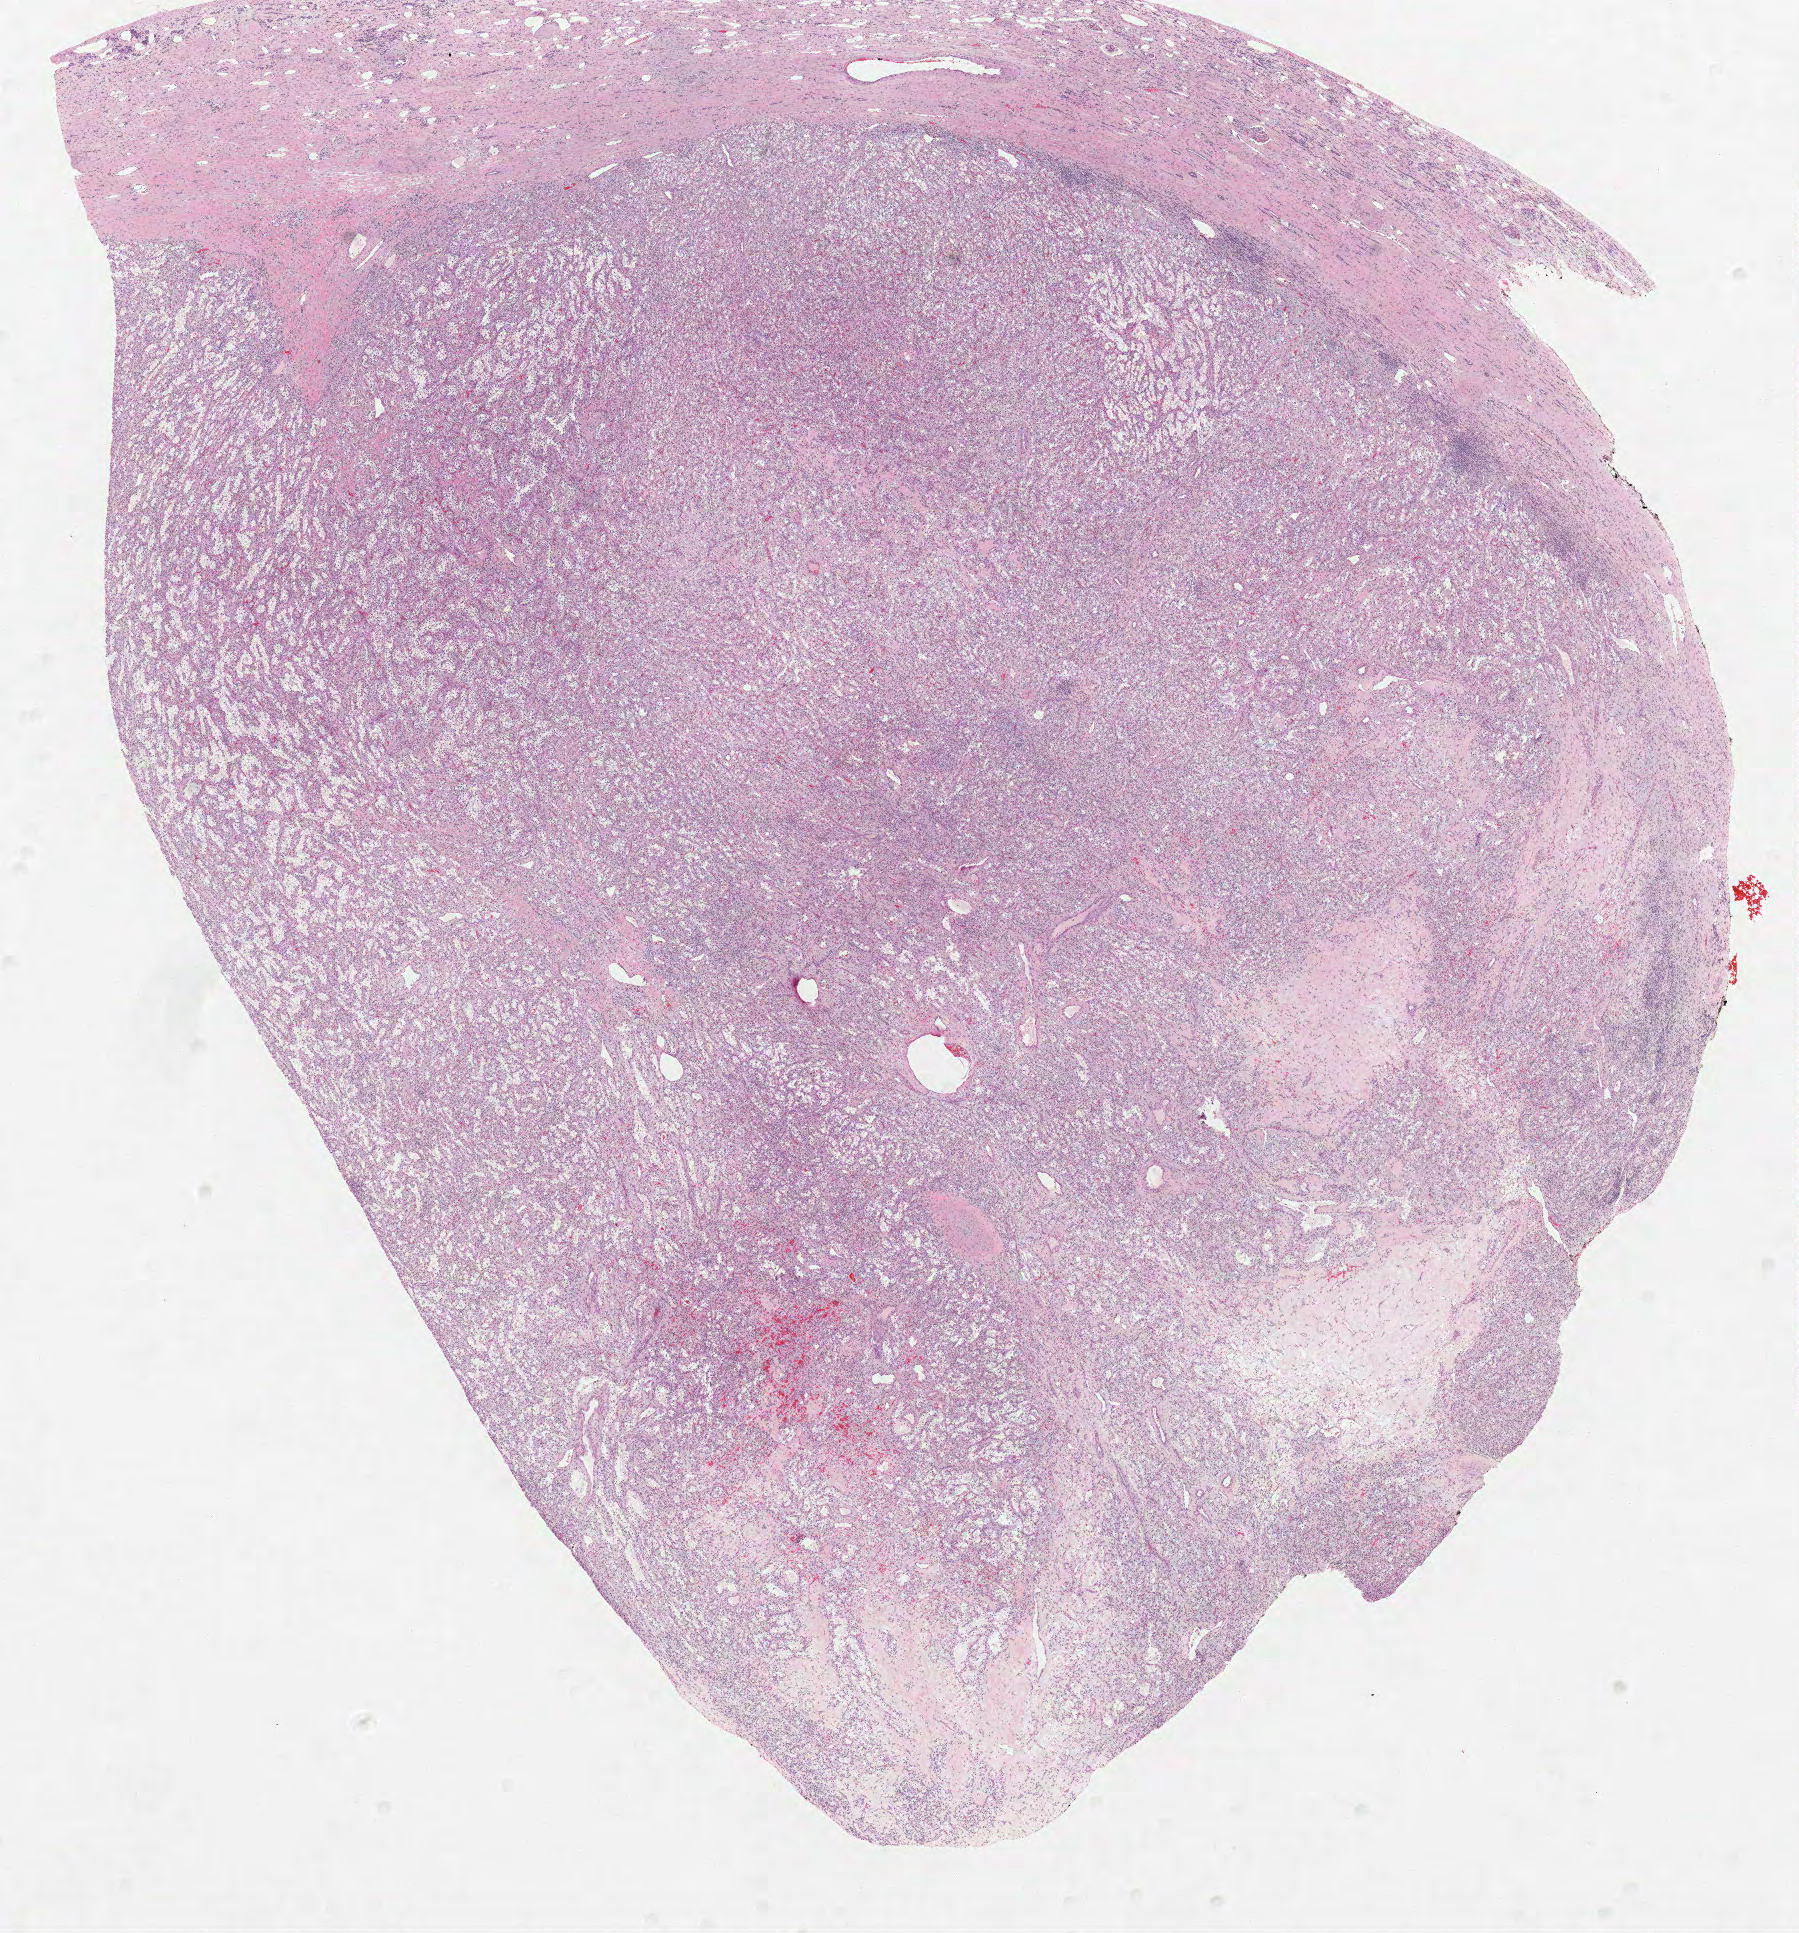
Digitized H&E tissue section (whole slide) — a low-resolution overview of the entire scanned area, about 14.4 x 15.5 mm (acquisition: 40x scan); formalin-fixed paraffin-embedded (FFPE) diagnostic section; sample: primary tumour, kidney. Male patient; age at initial diagnosis 53 years. Histologic grade: G2 (moderately differentiated).
Laterality: left. Diagnosis: Clear cell adenocarcinoma, NOS. AJCC pathologic stage: I.